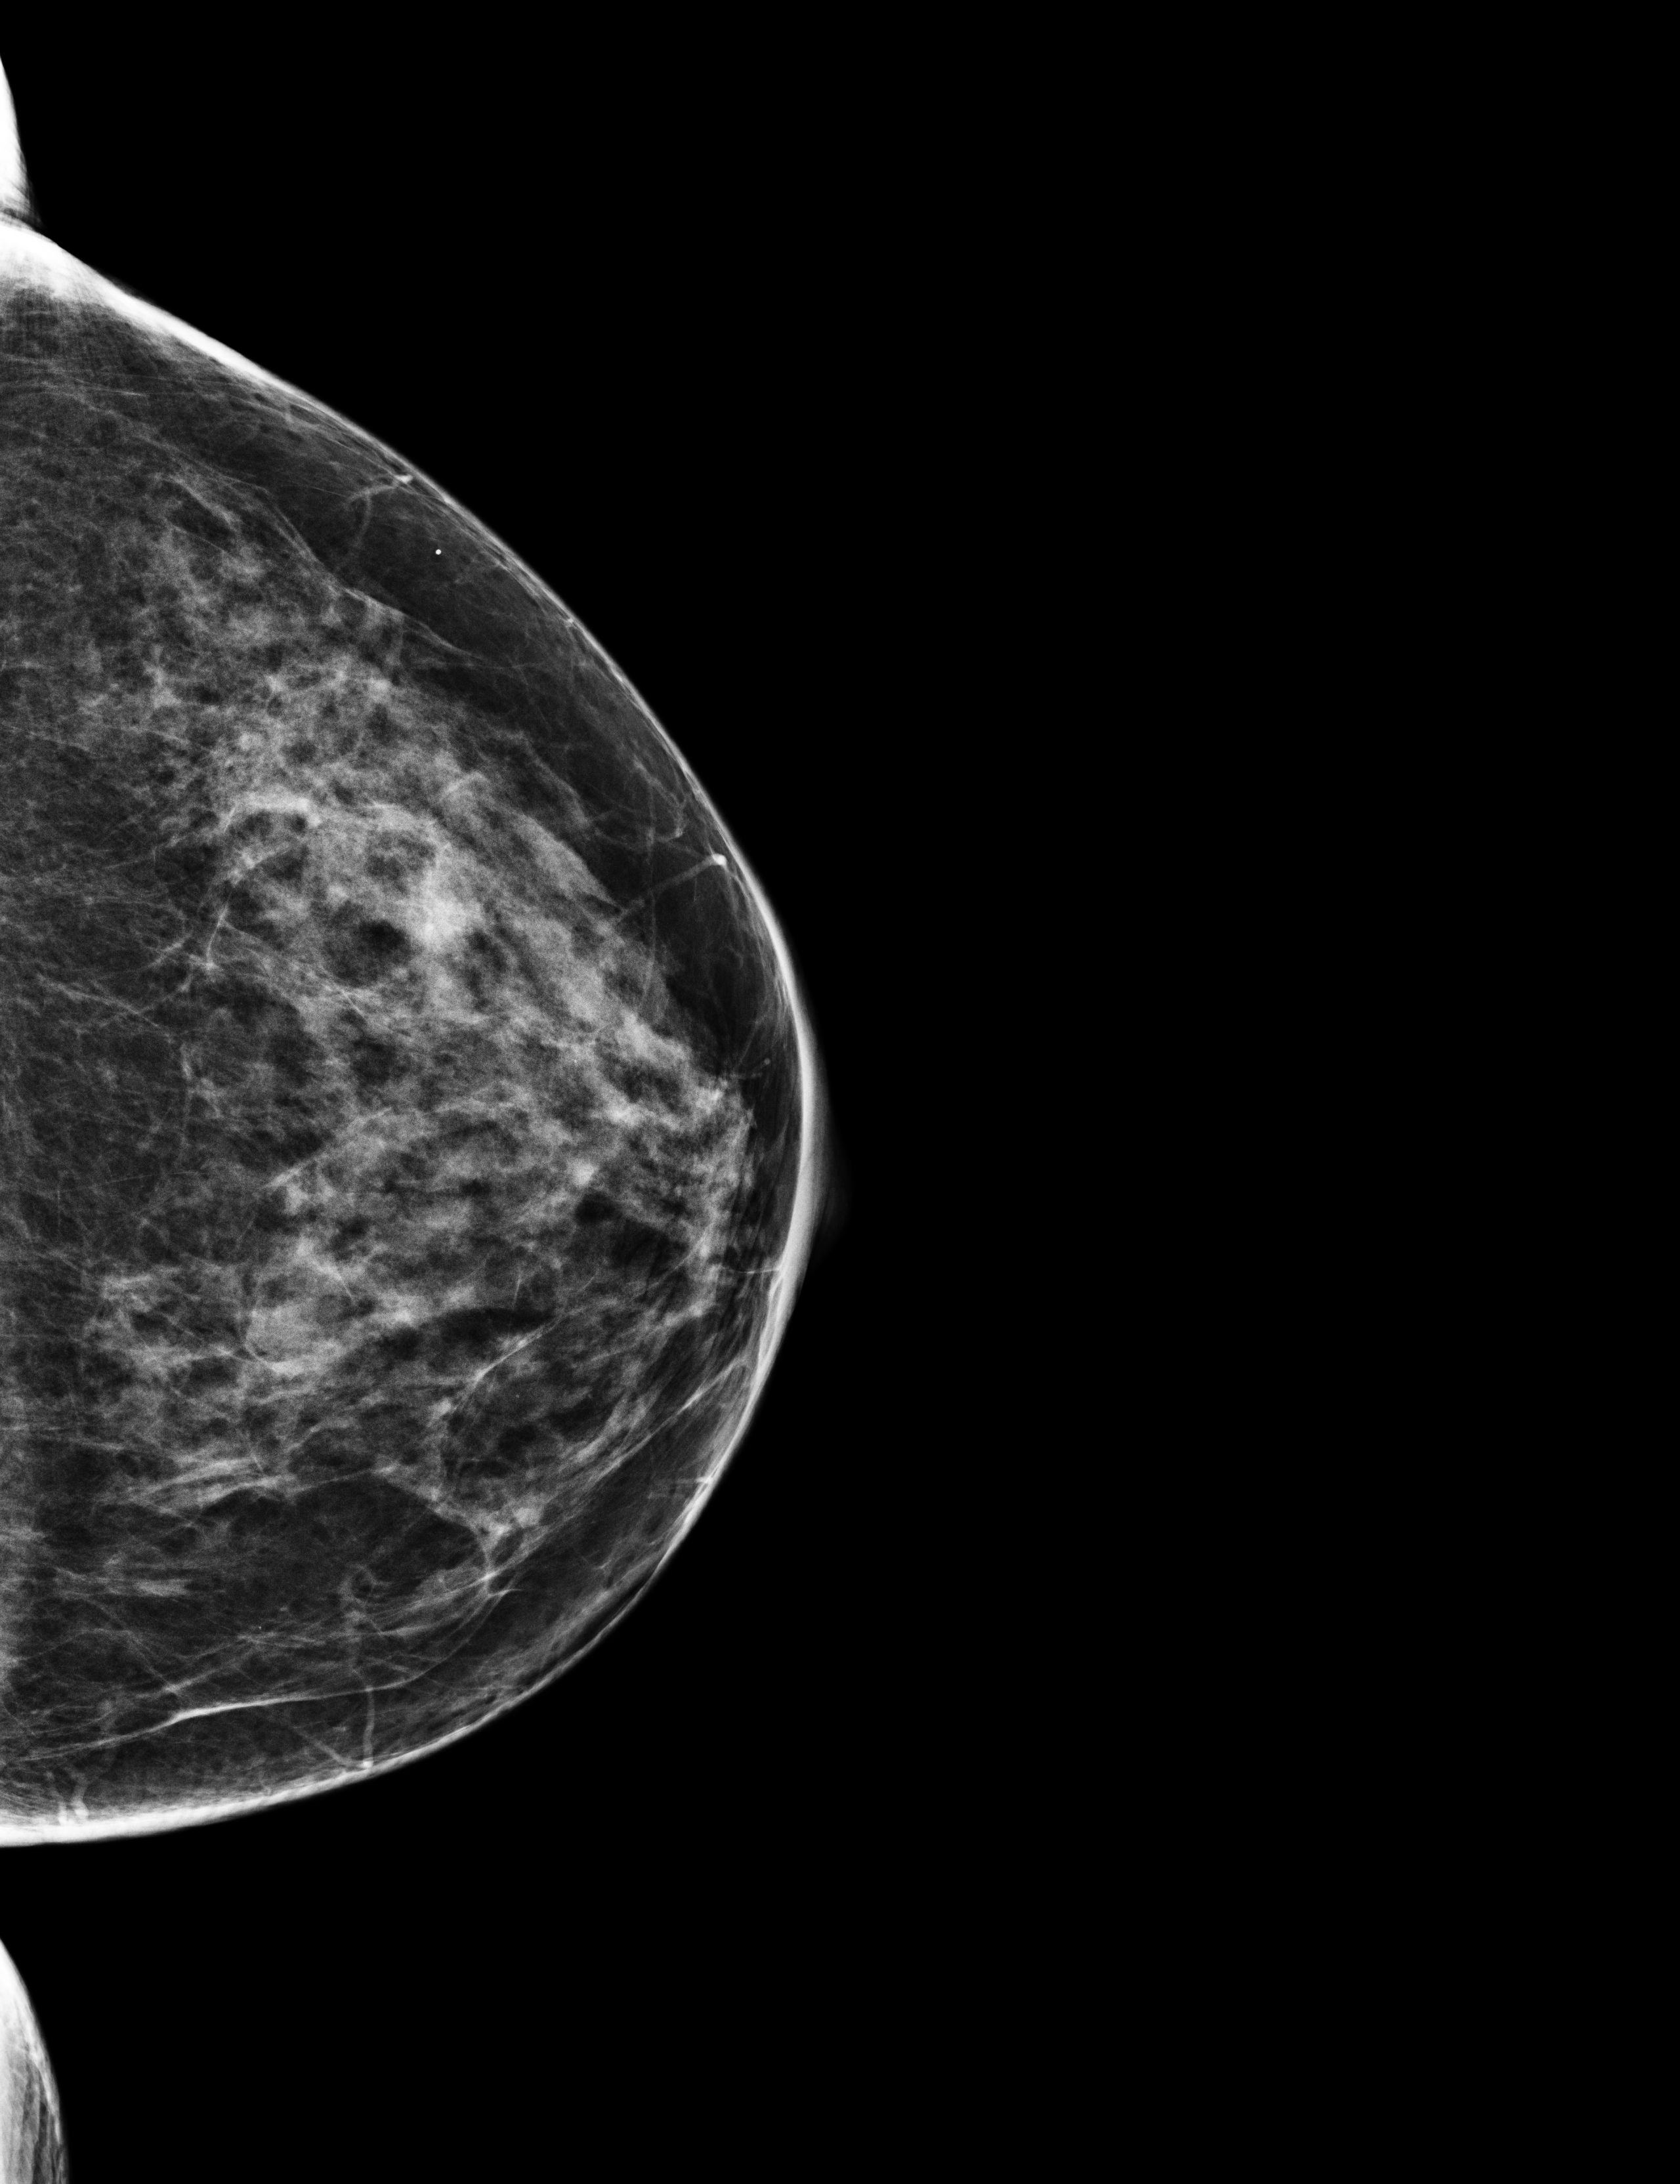
Annual screening mammography examination. Patient: female, 61 years.
Image type: full-field digital mammogram. Breast: left. Projection: CC view.